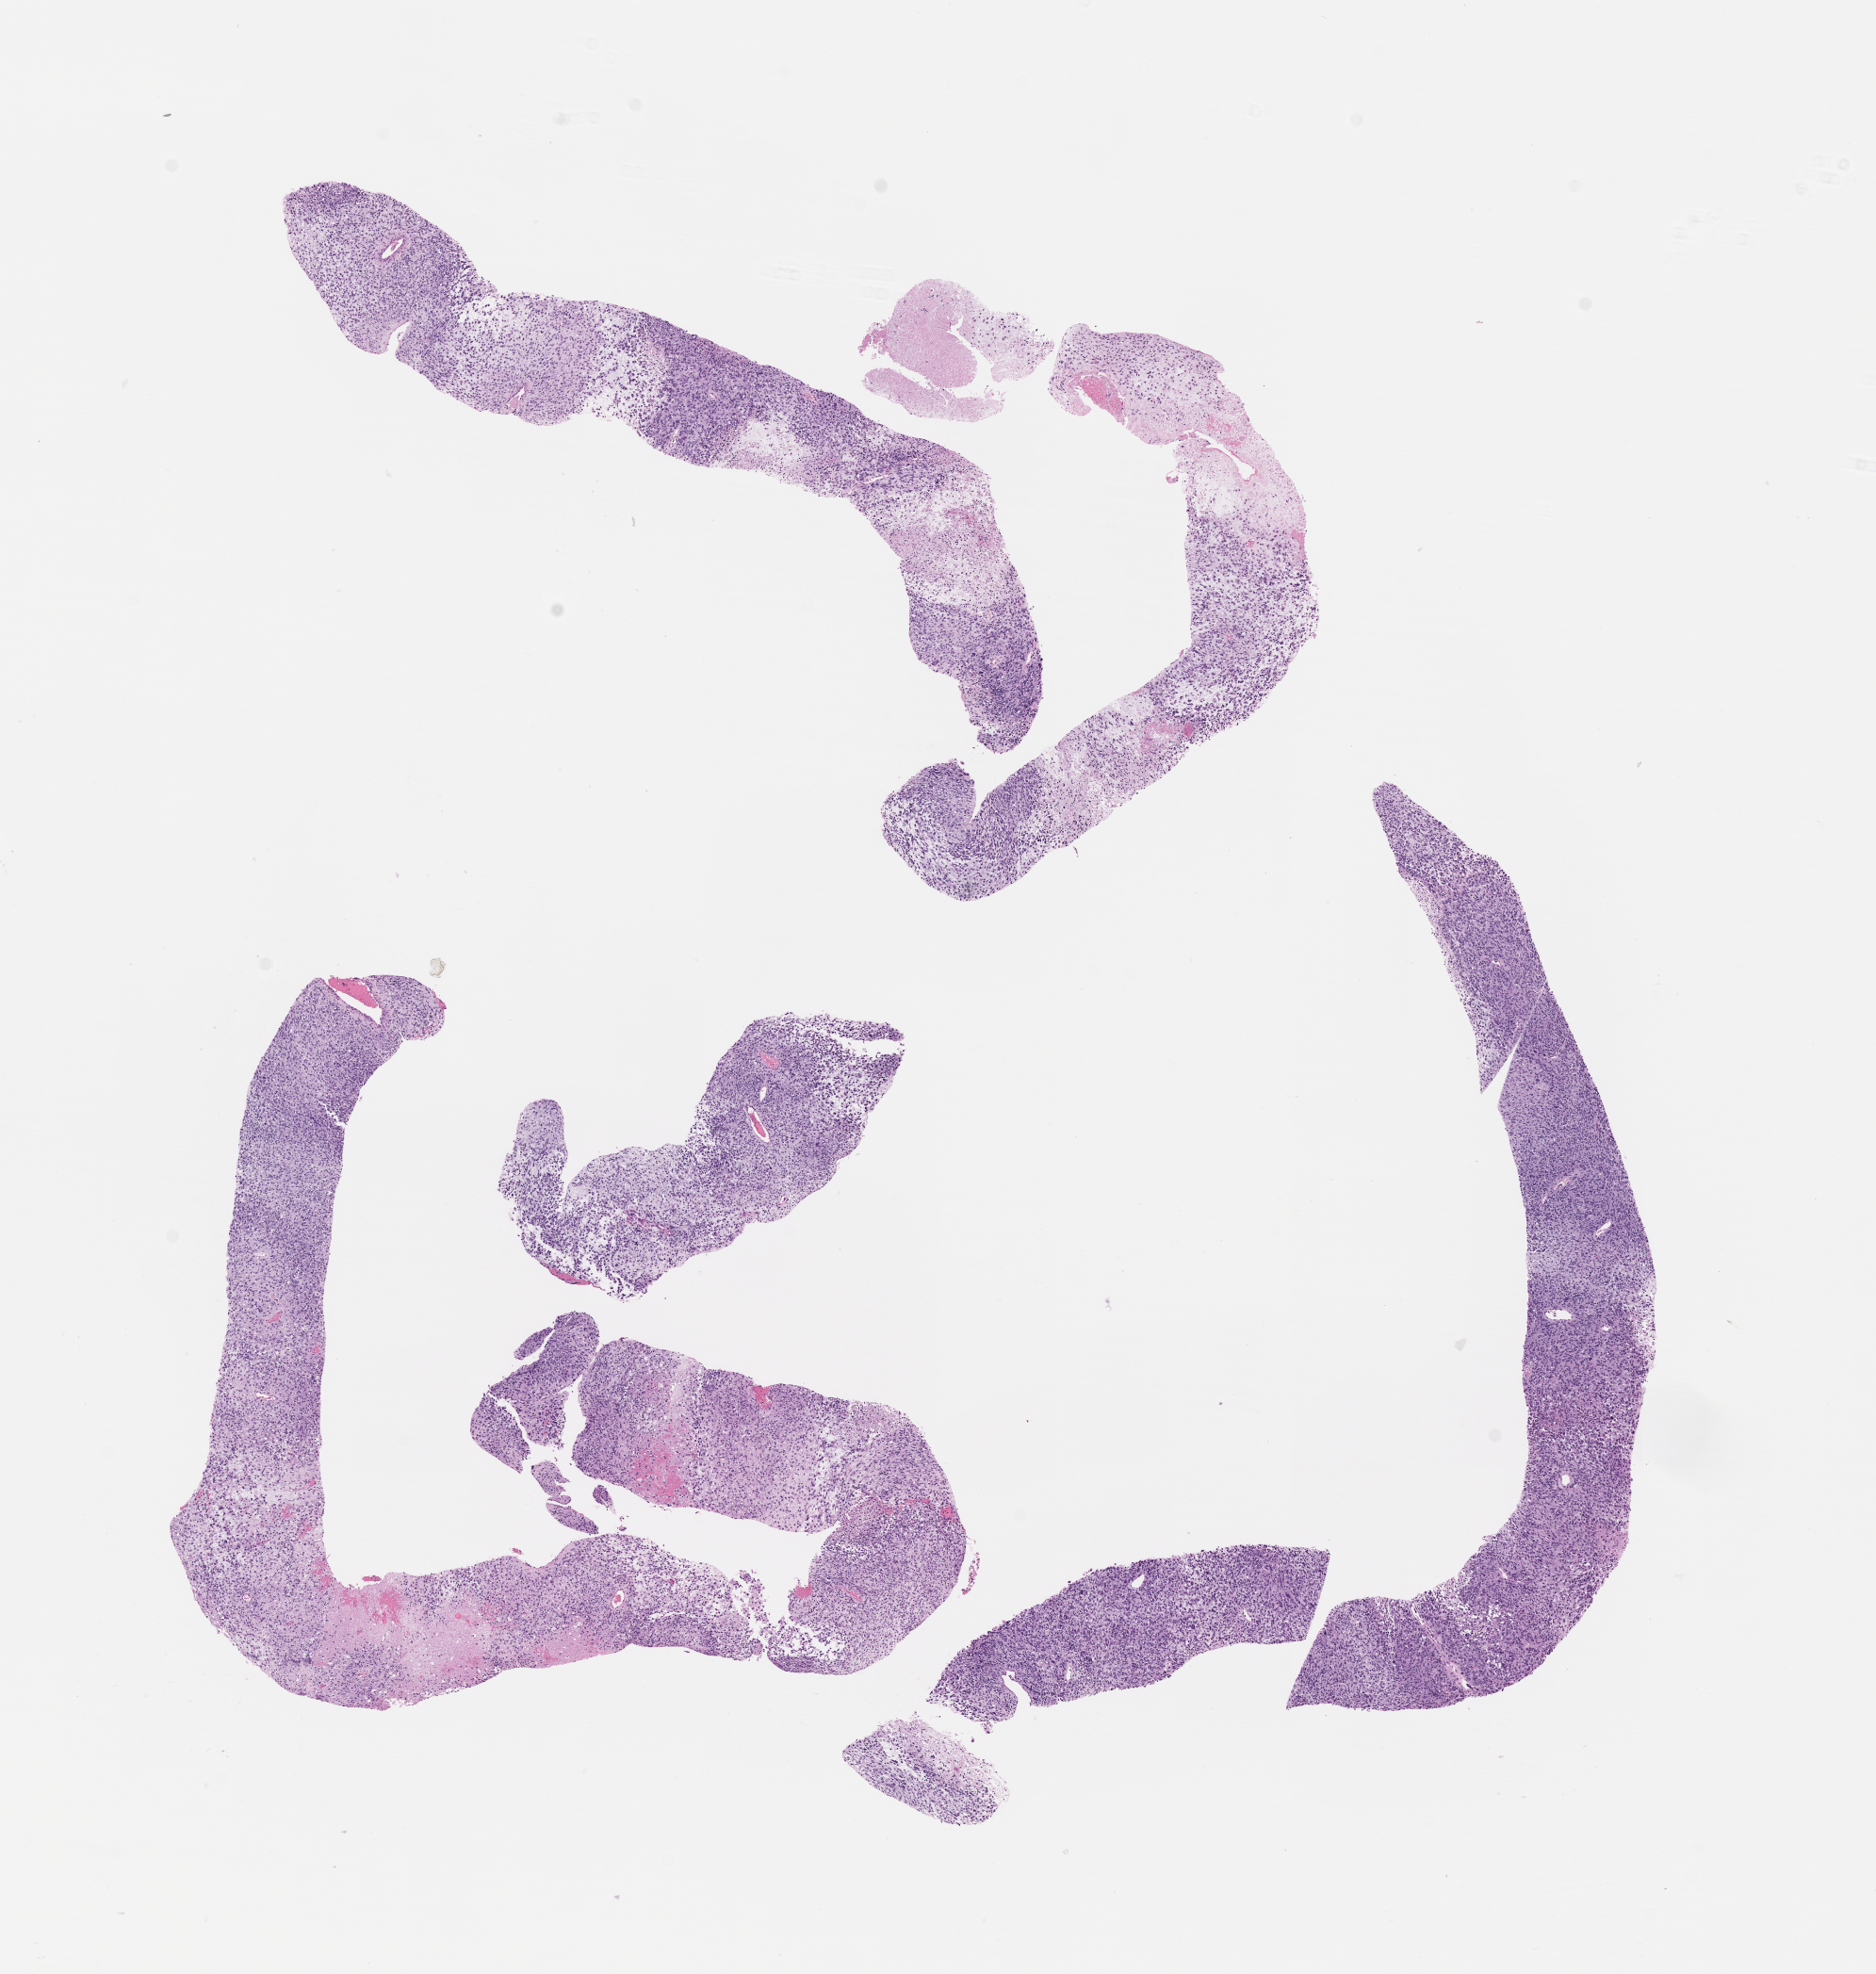
Whole-slide image, hematoxylin and eosin (H&E) stain of tumor tissue, a low-resolution overview of the entire scanned area, about 8.1 x 8.5 mm. FFPE section. Sample anatomic site: pelvis. Female patient, age at diagnosis 3.9 years.
- metastatic status at presentation (as recorded): non-metastatic
- diagnosis: rhabdomyosarcoma; histological classification: embryonal rhabdomyosarcoma
- stage (as recorded): 3